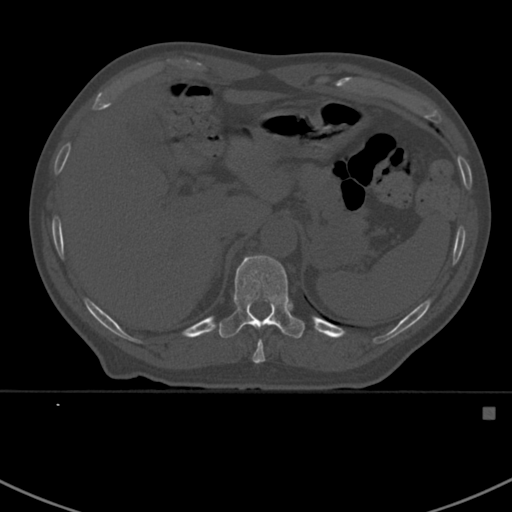
CT including the spine, one axial slice. Slice 352 of 412 in the series (ordered by position). 120 kVp. Bone window (W 1800 / L 400 HU). 1.5 mm slice thickness. 512 × 512 image matrix, field of view 358 × 358 mm. Patient: male, 59 years. Case-level facts recorded for this patient, not image findings: primary cancer: prostate.
Annotated regions visible in this slice (semi-automatic segmentation, software-assisted and operator-edited):
- T10 vertebra: bounding box [x1, y1, x2, y2] px = [252, 341, 265, 363]
- T11 vertebra: [219, 254, 305, 338]